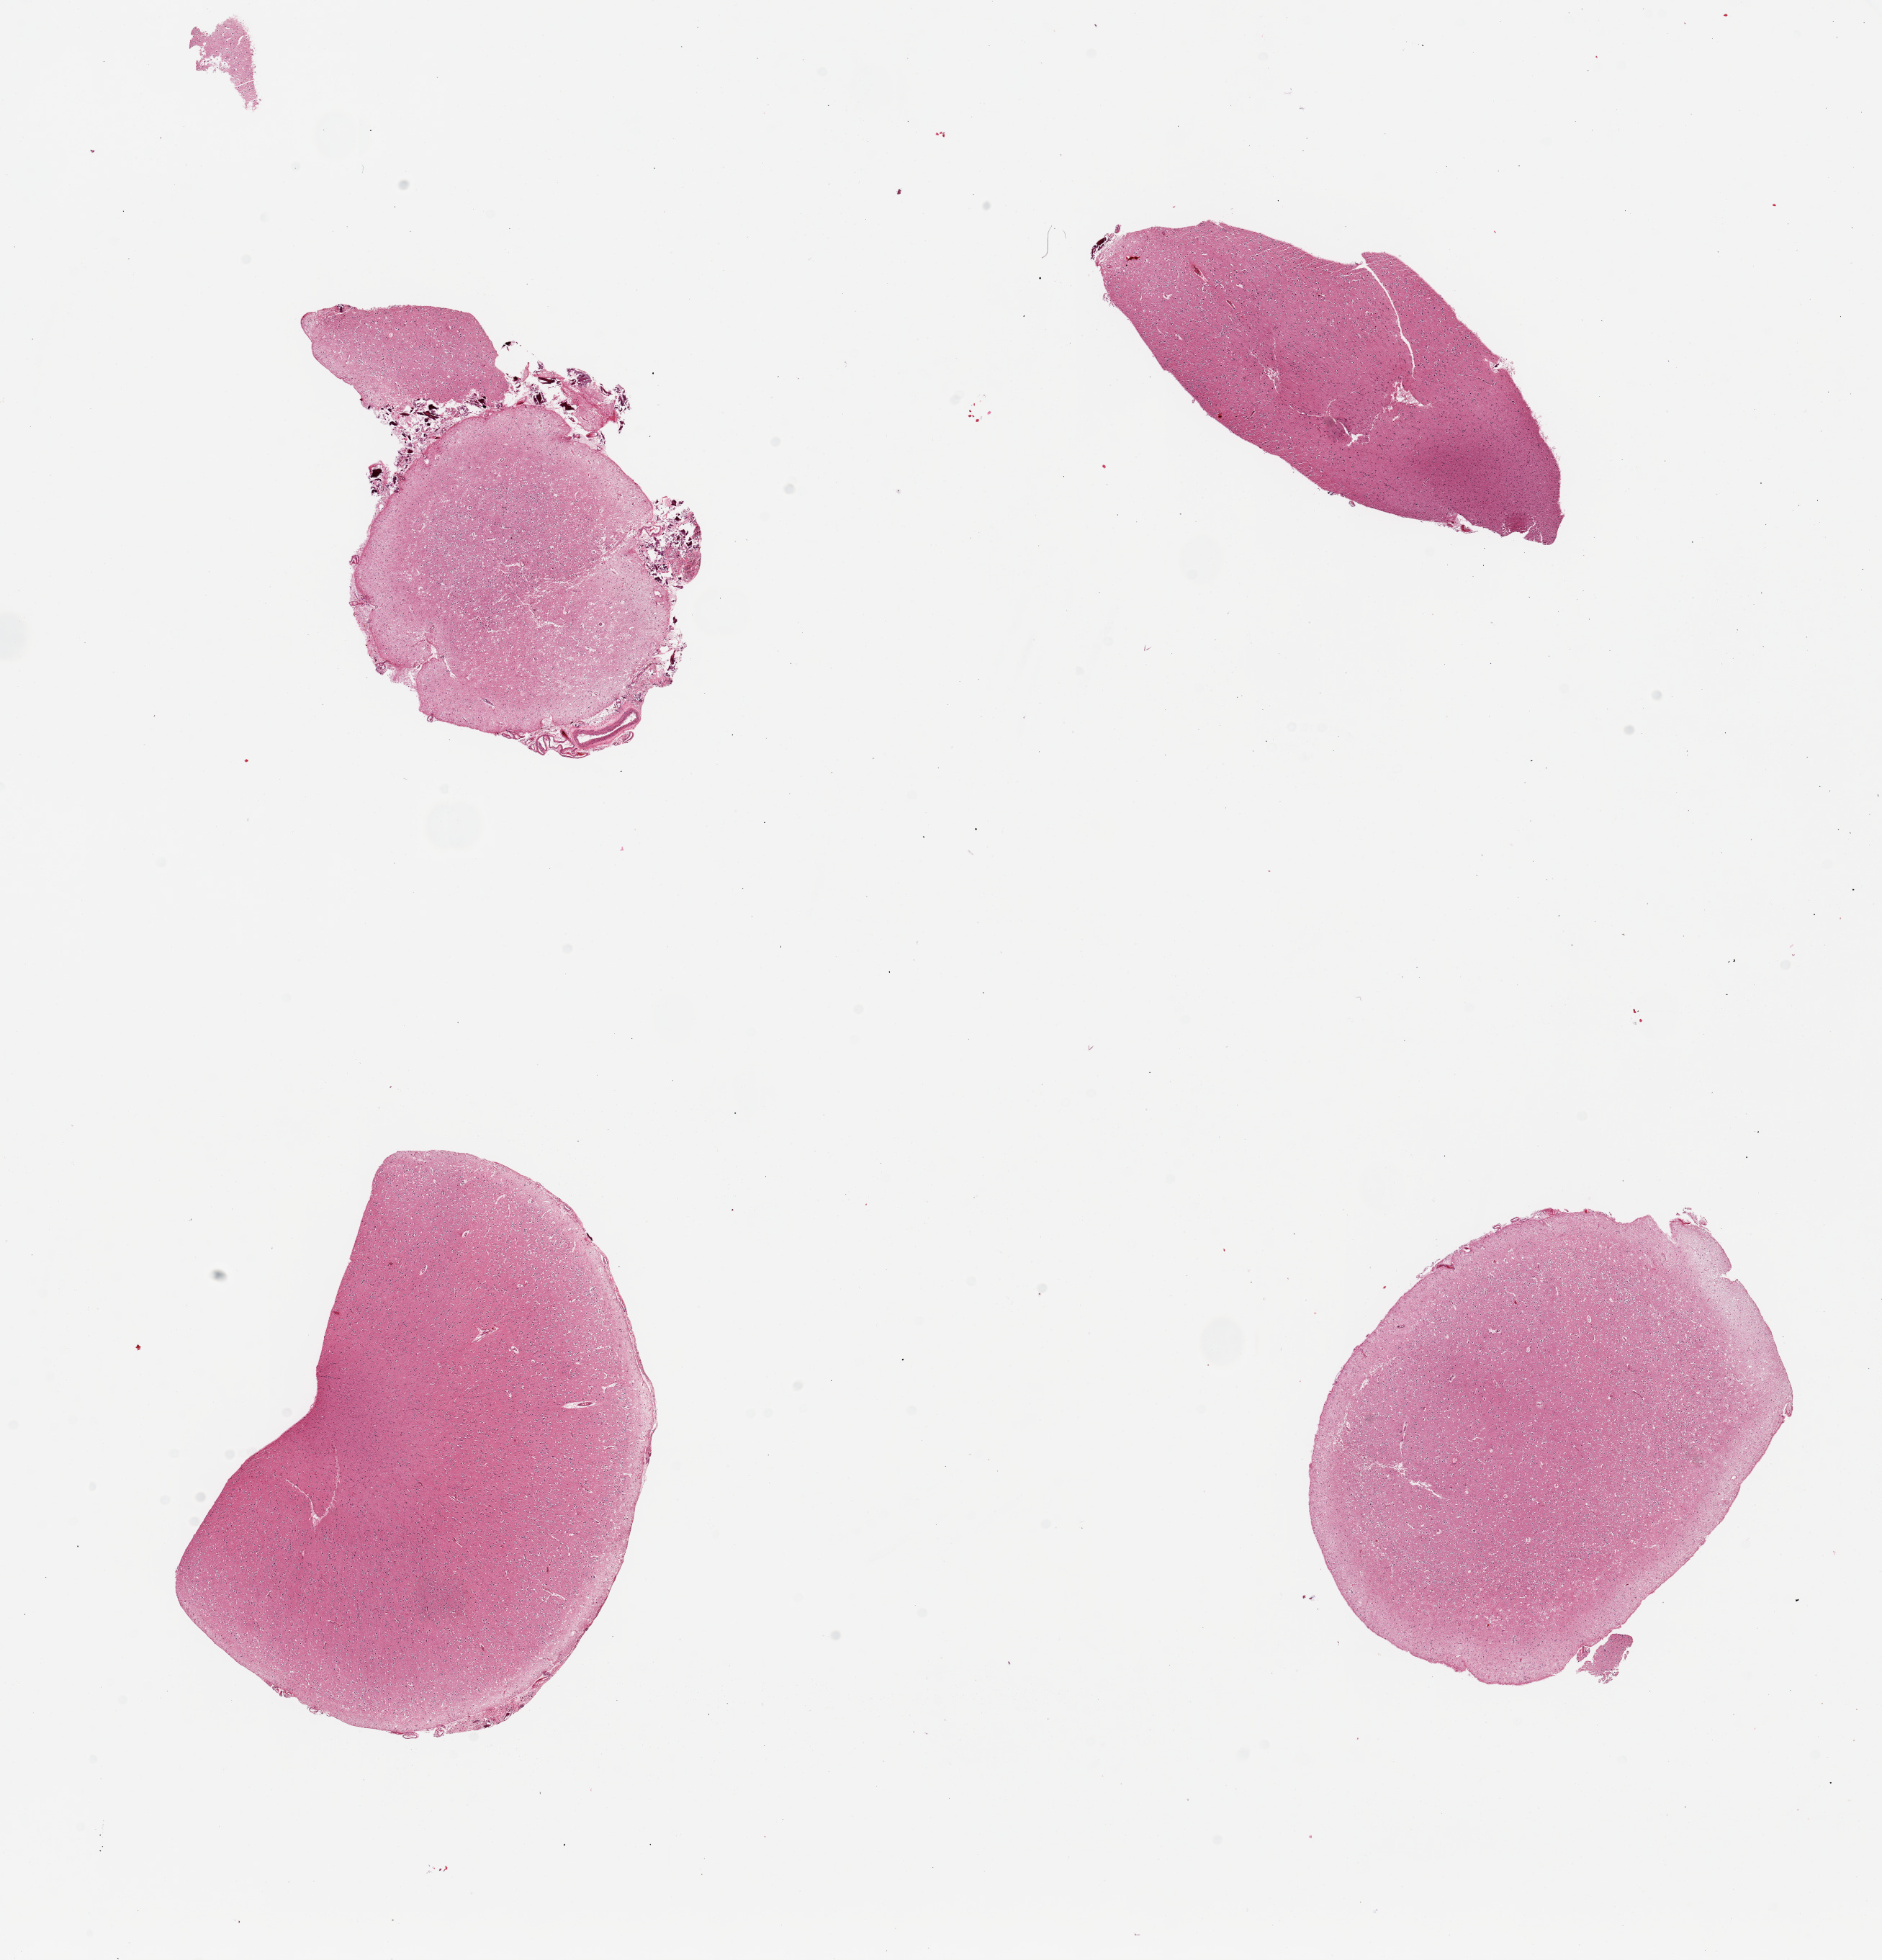
H&E whole-slide image, low-resolution overview of the scanned area, about 20.7 x 21.5 mm, PAXgene-fixed, paraffin-embedded tissue, target tissue: cerebral cortex, tissue donor sample. Donor sex: male.
Reviewer comment on this tissue sample: 4 pieces;focally meninges attached.